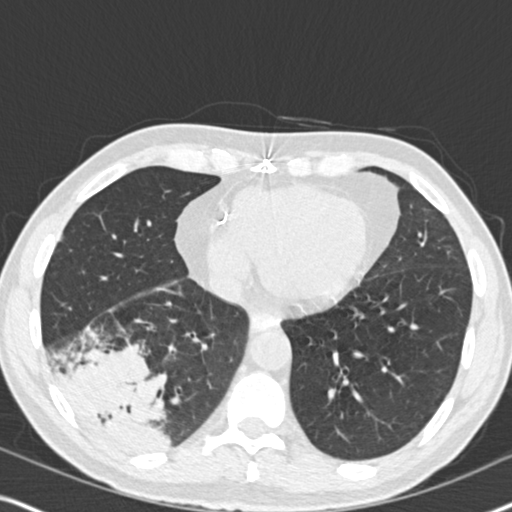
Low-dose screening chest CT, axial slice. Second screening round (one year after baseline). Lung window (W 1500 / L -600 HU). 2 mm slice thickness. Standard (soft-tissue) reconstruction kernel (B30f). 512 × 512 image matrix, field of view 330 × 330 mm. Male participant, aged 61 years at enrolment. Current smoker at enrolment.
• Expert reader's lesion annotation, bounding box <42,314,187,462> (left, top, right, bottom; pixels).
• Screening reader's record for this exam (one nodule recorded; not confirmed to be the boxed lesion): non-calcified nodule or mass ≥4 mm, right lower lobe, 90 × 80 mm, soft tissue attenuation, pre-existing on the prior screen: yes; interval growth: yes.
• Official screen result: positive, other.
• Later outcome: lung cancer diagnosed 20 days after this screen — bronchiolo-alveolar adenocarcinoma, NOS, right lower lobe, moderately differentiated (G2), stage IIIB (AJCC 6th edition), 90 mm at pathology.